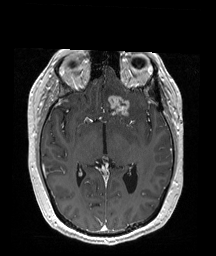
Brain MRI from a brain-tumour surgery series, one axial slice; position 104 of 192 along the scan axis; T1-weighted post-contrast; 1 mm slice thickness; 216 × 256 image matrix, field of view 211 × 250 mm. From the clinical record (not read from this slice): histopathology: Oligodendroglioma; WHO grade: 2.
Structures marked on this image (manually delineated by an expert):
- tumour: box from (x=107, y=95) to (x=132, y=117) px